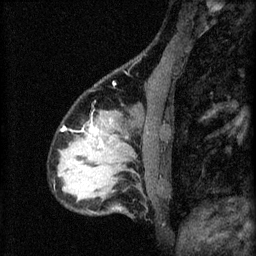
Breast MRI (dynamic contrast-enhanced), one sagittal slice; position 19 of 60 along the scan axis; 3 images stored at this slice position (order not interpretable as contrast timing); 1.5 T; TE 4.2 ms, TR 8.2 ms; 256 × 256 image matrix, field of view 180 × 180 mm. Patient: female, 37 years.
Structures marked on this image (semi-automatically segmented with operator editing):
- analysis volume of interest (the breast-tissue region the enhancement analysis was run in; not a lesion): box from (x=67, y=120) to (x=122, y=179) px
- tumour enhancement mask (voxels above the 70 % enhancement threshold inside the analysis volume of interest): (x=90, y=128)–(x=98, y=133)